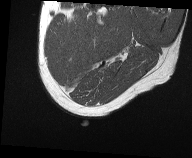
MRI of an extremity soft-tissue mass, one axial slice; slice 5 of 61 in the series (ordered by position); MR volume resampled by the dataset authors to the PET/CT grid (not the native acquisition matrix); 192 × 158 image matrix. Male patient. Case-level facts recorded for this patient, not image findings: histological type: pleiomorphic liposarcoma; grade: high; site of the primary tumour: left thigh.
Outlined on this slice (expert contour drawn on MRI and transferred to this co-registered scan by the dataset authors):
- gross tumour volume including surrounding oedema: box from (x=80, y=21) to (x=108, y=36) px